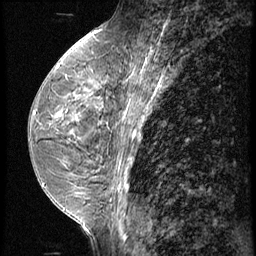
Breast MRI (dynamic contrast-enhanced), one sagittal slice. Slice 26 of 62 in the series (ordered by position). 3 images stored at this slice position (order not interpretable as contrast timing). 1.5 T. TE 4.2 ms, TR 9 ms. 256 × 256 image matrix. Female patient, age 44 years. Case-level facts recorded for this patient, not image findings: setting: breast cancer imaged before/during neoadjuvant chemotherapy; receptor status: triple-negative.
Structures marked on this image (semi-automatic segmentation, software-assisted and operator-edited):
- analysis volume of interest (the breast-tissue region the enhancement analysis was run in; not a lesion): box from (x=67, y=64) to (x=116, y=125) px
- tumour enhancement mask (voxels above the 140 % enhancement threshold inside the analysis volume of interest): (x=74, y=96)–(x=87, y=112)